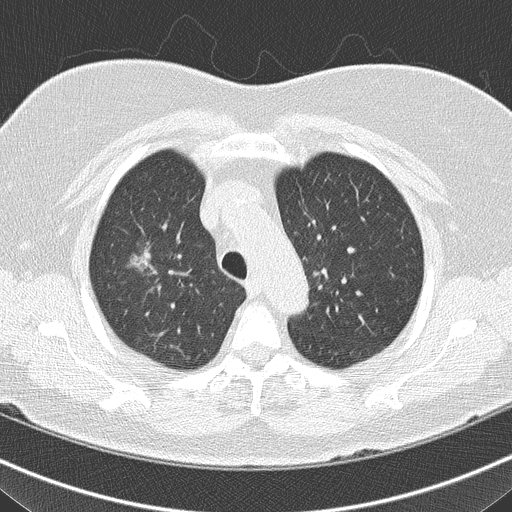
Chest CT (low-dose screening protocol), one axial image. Third annual screen. Lung window (W 1500 / L -600 HU). 2 mm slice thickness. Lung (sharp) reconstruction kernel (B50f). 512 × 512 image matrix. Female, age 74 years at enrolment. Former smoker at enrolment.
• Lesion marked by an expert reader, box from (x=111, y=234) to (x=179, y=296) px.
• The screening reader recorded 5 non-calcified nodules or masses ≥4 mm on this exam (right upper lobe, right middle lobe, right middle lobe, left lower lobe, right lower lobe); which of them this box marks is not recorded.
• Lung cancer was diagnosed 117 days after this screen: bronchiolo-alveolar carcinoma, non-mucinous, right upper lobe, well differentiated (G1), stage IA (AJCC 6th edition), 14 mm at pathology.